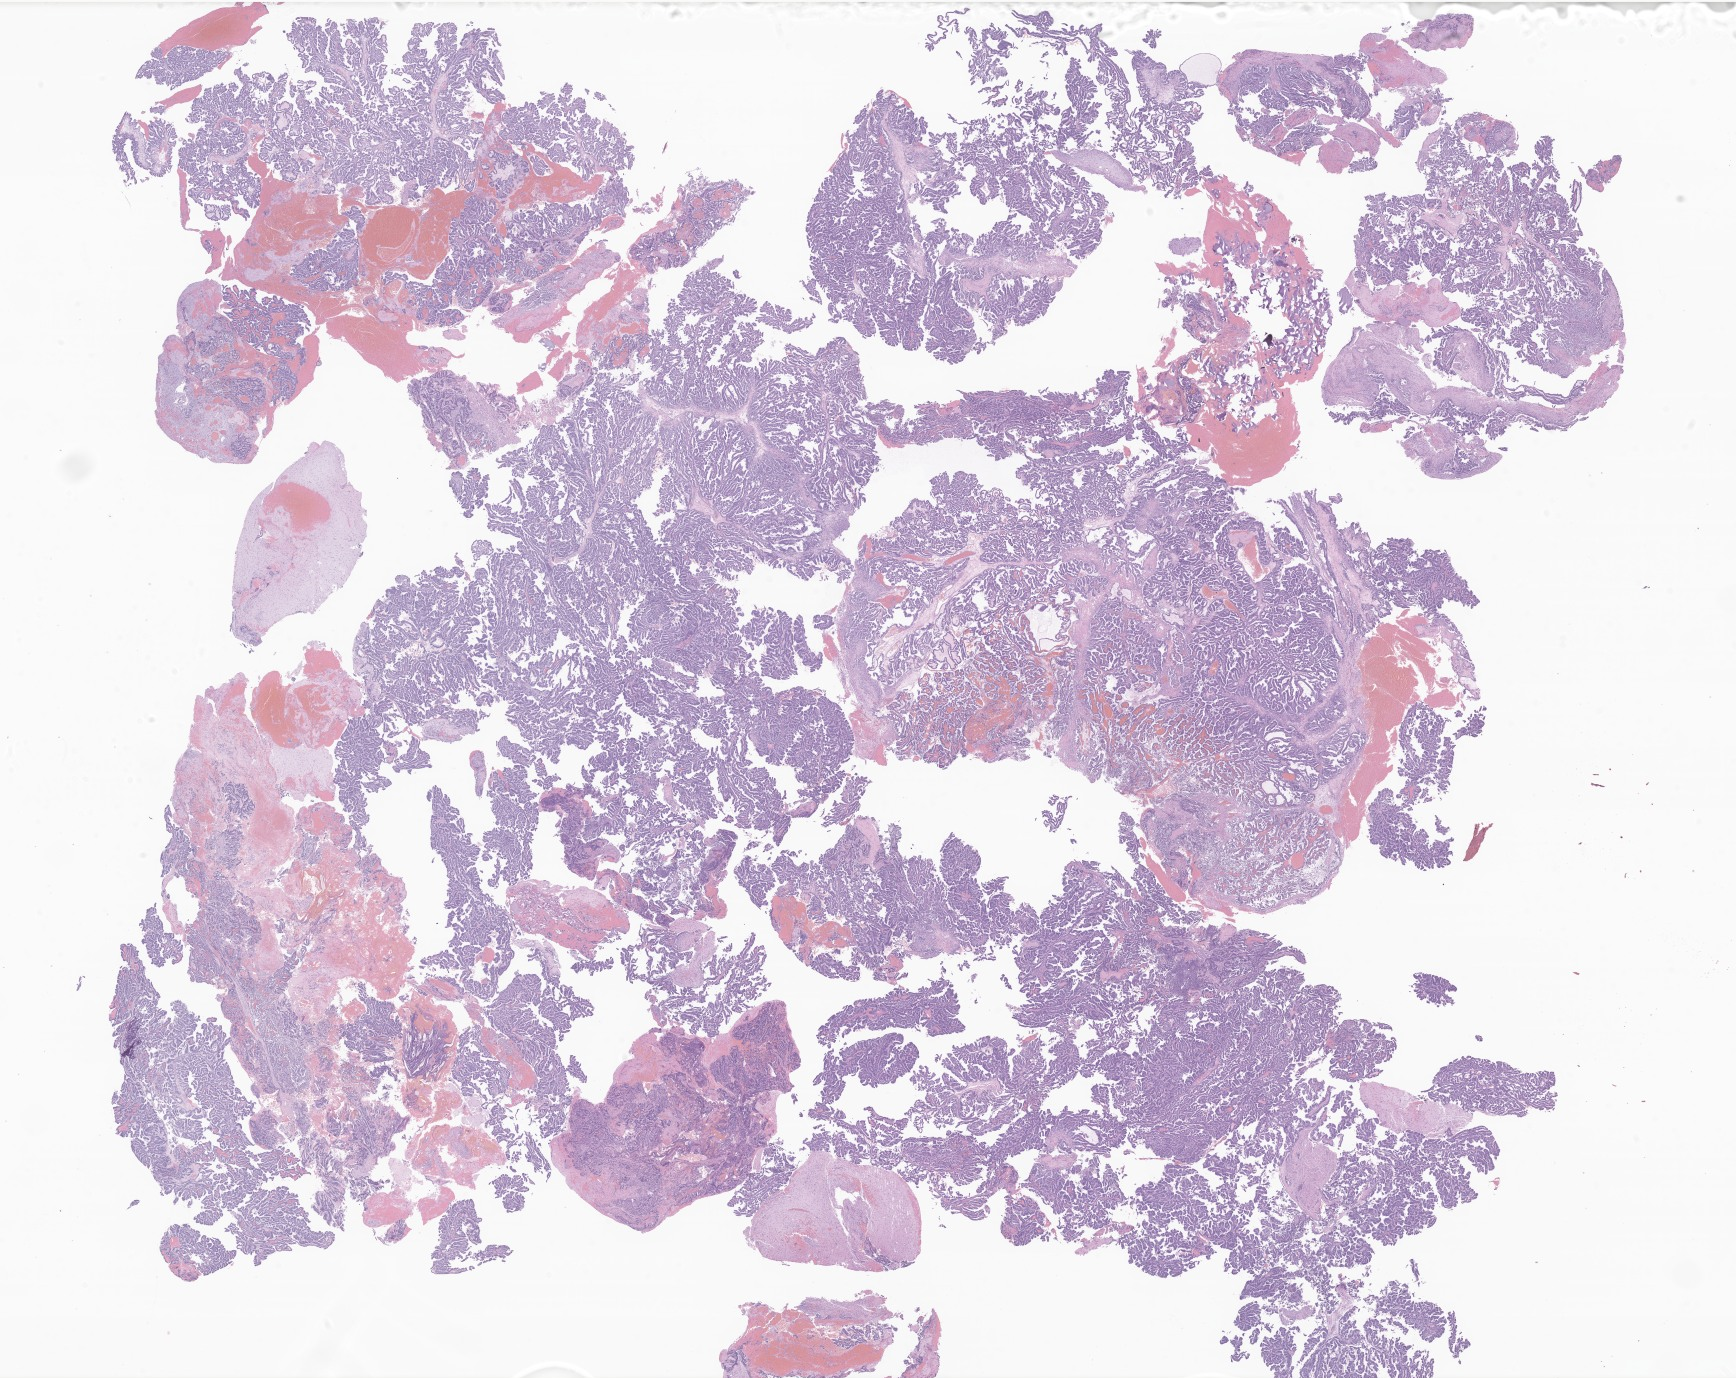
Digitized haematoxylin and eosin-stained section of tumor tissue from the brain, shown as a low-resolution overview of the whole scanned area (about 29.3 x 23.2 mm); formalin-fixed, paraffin-embedded (FFPE) tissue. Patient female; age 566 days.
Diagnosis (ICD-O-3 morphology term): Choroid plexus carcinoma.